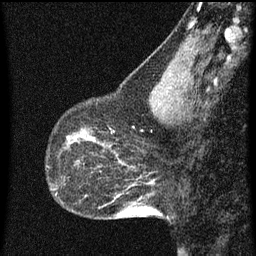
Breast MRI (dynamic contrast-enhanced), one sagittal slice. Position 21 of 60 along the scan axis. Dynamic contrast-enhanced series, image 2 of 3 at this slice position (ordered by acquisition). 1.5 T. TE 4.2 ms, TR 8 ms. 2 mm slice thickness. 256 × 256 image matrix. Female patient, age 43 years.
Annotated regions visible in this slice (semi-automatically segmented with operator editing):
- analysis volume of interest (the breast-tissue region the enhancement analysis was run in; not a lesion): bounding box (x1, y1, x2, y2) in pixels: (53, 104, 101, 151)
- tumour enhancement mask (voxels above the 70 % enhancement threshold inside the analysis volume of interest): (68, 136, 99, 145)